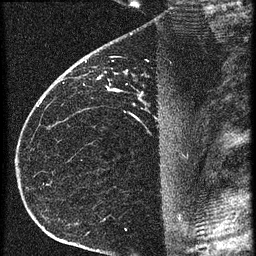
Breast MRI (dynamic contrast-enhanced), one sagittal slice; position 41 of 60 along the scan axis; 3 images stored at this slice position (order not interpretable as contrast timing); 1.5 T; TE 4.2 ms, TR 20.4 ms; 1.5 mm slice thickness; 256 × 256 image matrix, field of view 180 × 180 mm. Female patient, age 35 years. From the clinical record (not read from this slice): setting: breast cancer imaged before/during neoadjuvant chemotherapy; receptor status: HR-positive, HER2-negative.
Annotated regions visible in this slice (semi-automatically segmented with operator editing):
- analysis volume of interest (the breast-tissue region the enhancement analysis was run in; not a lesion): bounding box <65,60,169,119> (left, top, right, bottom; pixels)
- tumour enhancement mask (voxels above the 90 % enhancement threshold inside the analysis volume of interest): <84,60,116,91>